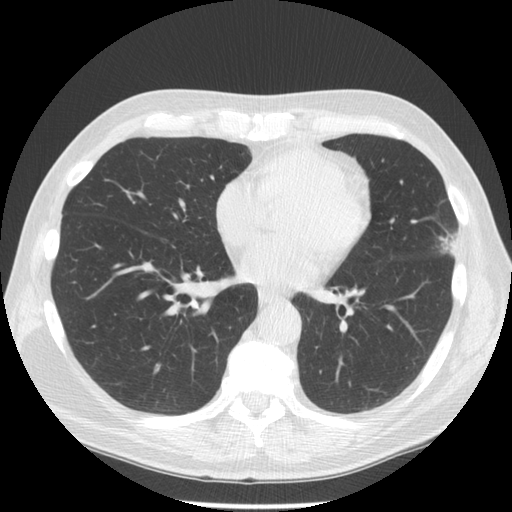
Low-dose screening chest CT, one axial slice; position 62 of 134 along the scan axis; reconstruction kernel STANDARD; 120 kVp; lung window (W 1500 / L -600 HU); 512 × 512 image matrix.
Annotated regions visible in this slice (expert manual segmentation):
- lesion 1 (tumor, upper lobe of left lung): bounding box (x1, y1, x2, y2) in pixels: (438, 234, 458, 255)